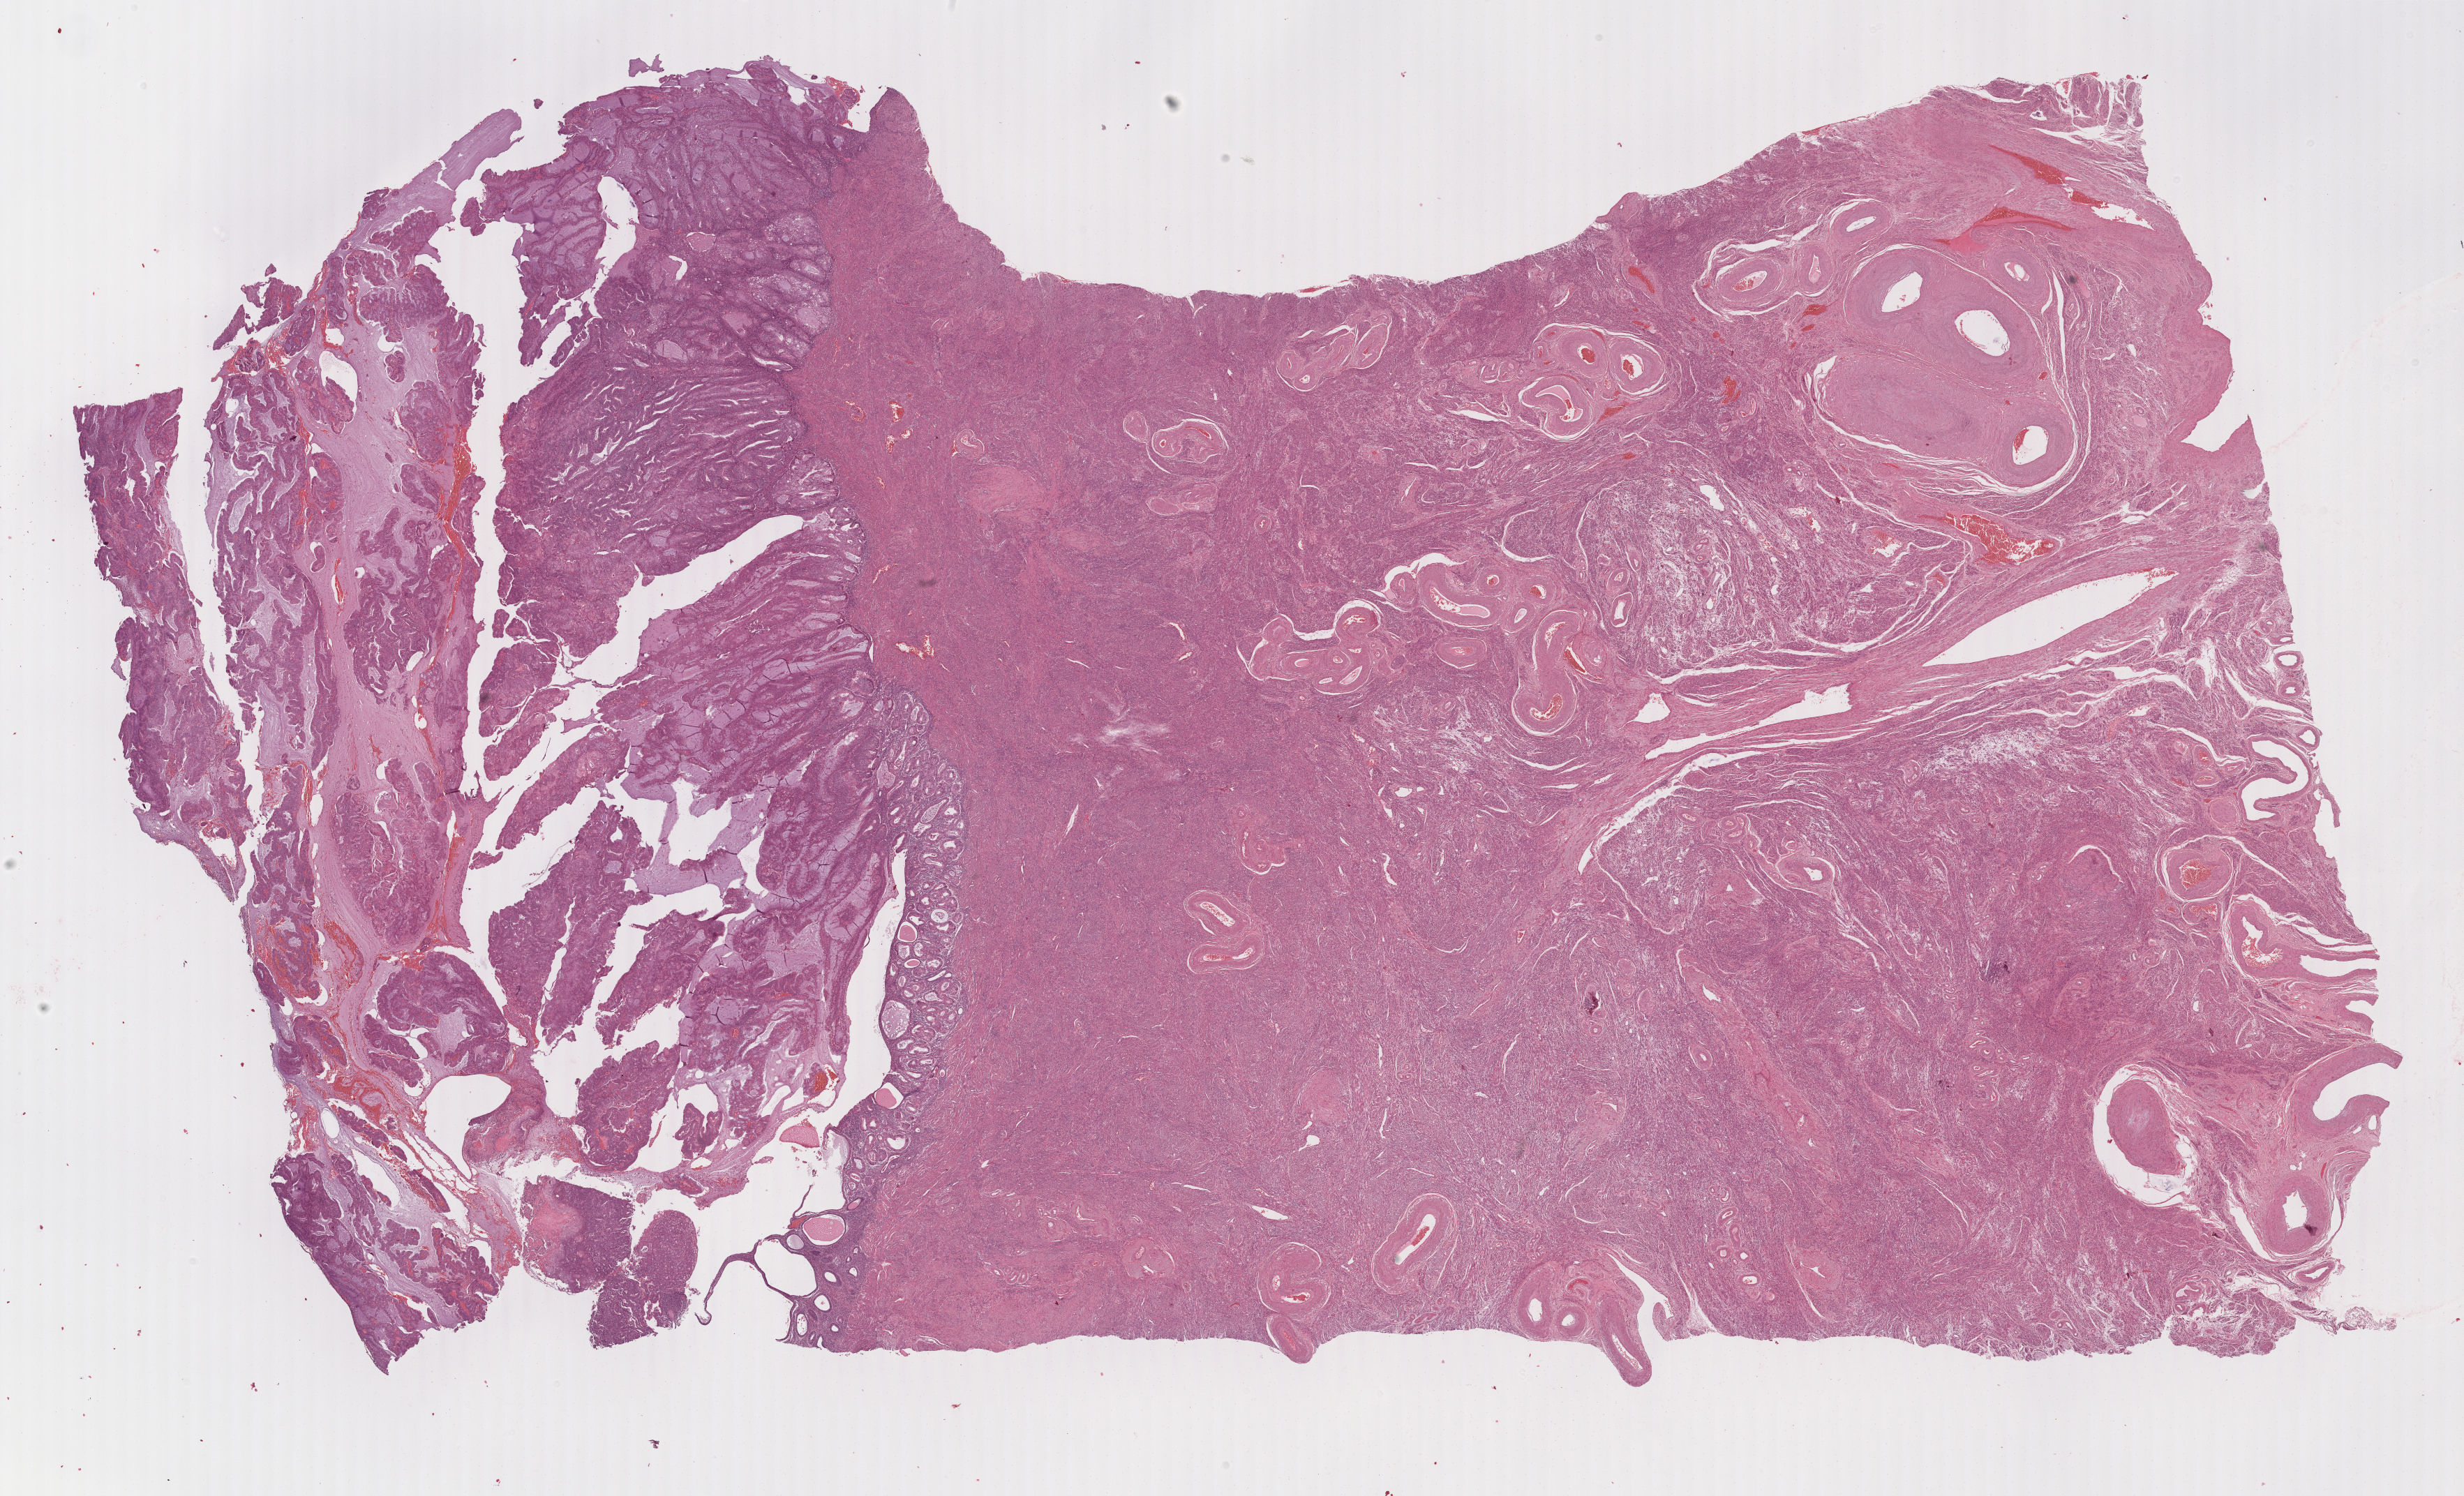
H&E whole-slide image, whole scanned area (about 28.1 x 17.0 mm, acquisition: 40x scan) shown as a low-resolution overview. Formalin-fixed paraffin-embedded (FFPE) diagnostic section. Sample: primary tumour, uterus. Female, age 69 years at initial diagnosis. Histologic grade: G1 (well differentiated).
Pathologic diagnosis: Endometrioid adenocarcinoma, NOS (fundus uteri). FIGO stage: IB.